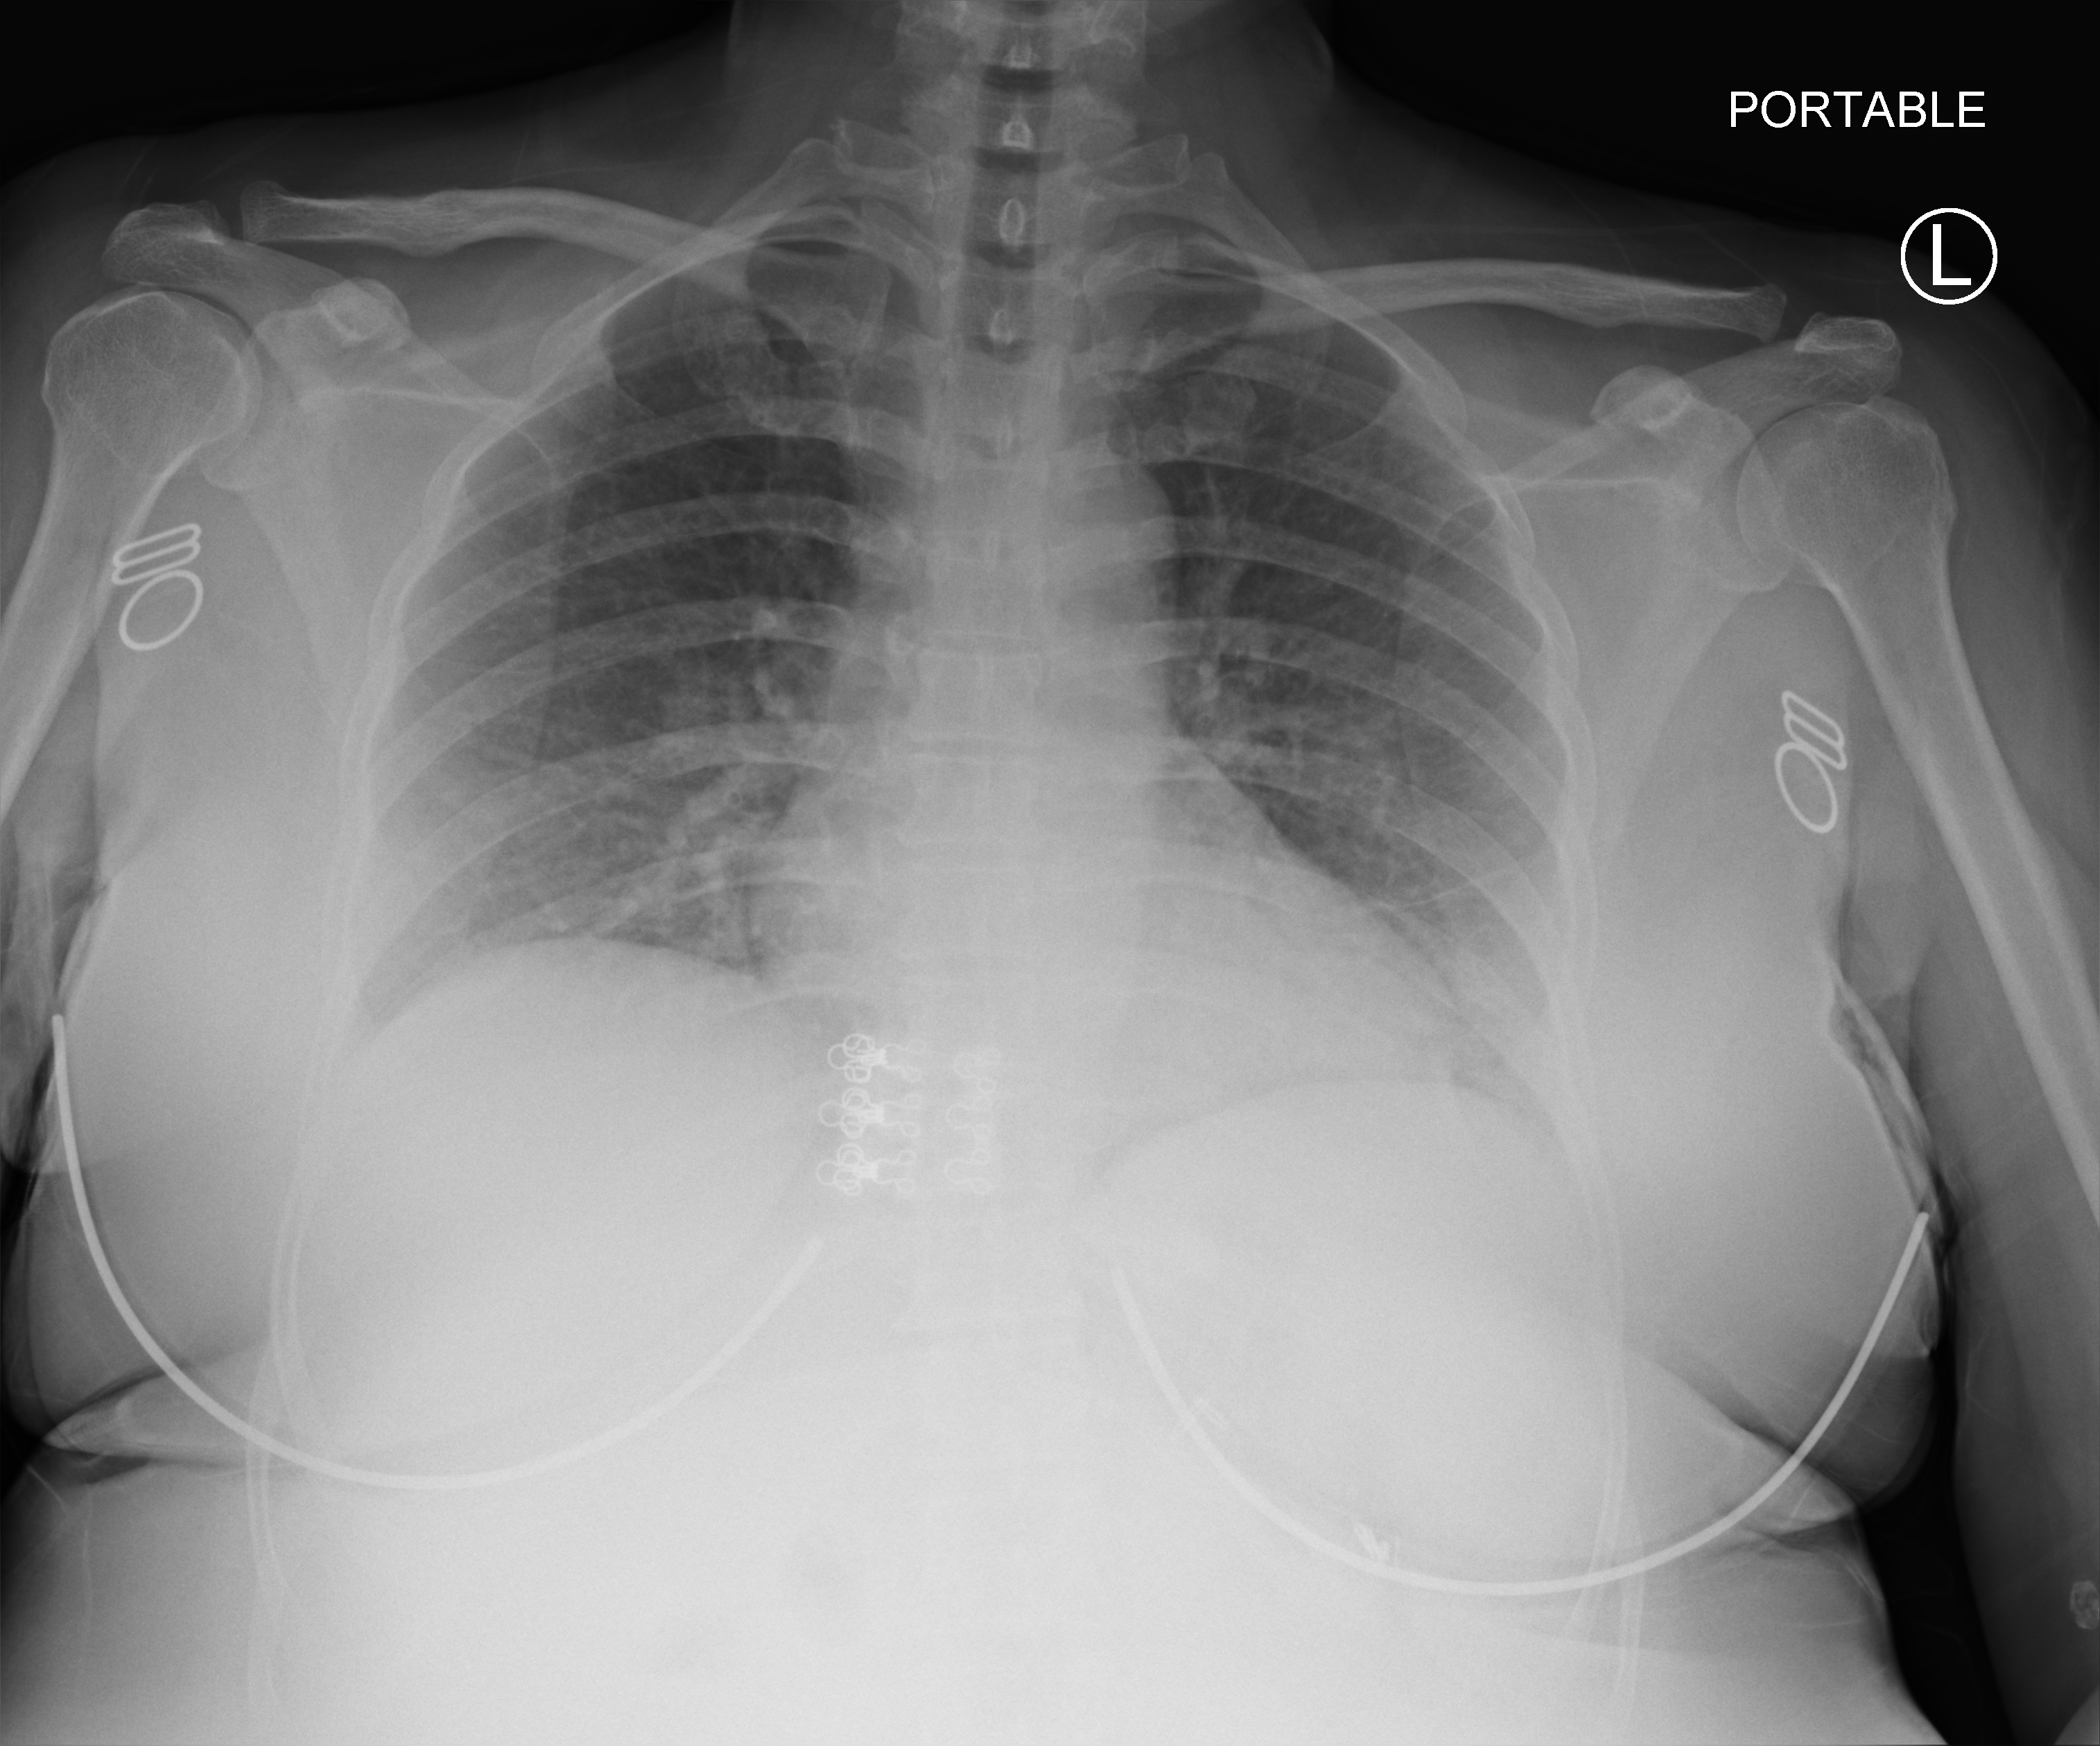
Bedside chest radiograph (computed radiography), anteroposterior (AP) projection. Patient hospitalised with COVID-19; female, aged 18–59 years.
Hospital-stay facts (about this admission, not read from this image; timing relative to this image not recorded): admitted to intensive care during this hospital stay: no.